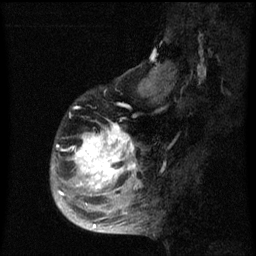
Breast MRI (dynamic contrast-enhanced), one sagittal slice; position 19 of 60 along the scan axis; dynamic contrast-enhanced series, image 2 of 3 at this slice position (ordered by acquisition); 1.5 T; TE 4.2 ms, TR 8 ms; 2 mm slice thickness; 256 × 256 image matrix, field of view 190 × 190 mm. Patient: female, 50 years.
Outlined on this slice (semi-automatically segmented with operator editing):
- analysis volume of interest (the breast-tissue region the enhancement analysis was run in; not a lesion): bounding box (x1, y1, x2, y2) in pixels: (51, 100, 142, 216)
- tumour enhancement mask (voxels above the 70 % enhancement threshold inside the analysis volume of interest): (58, 122, 136, 208)